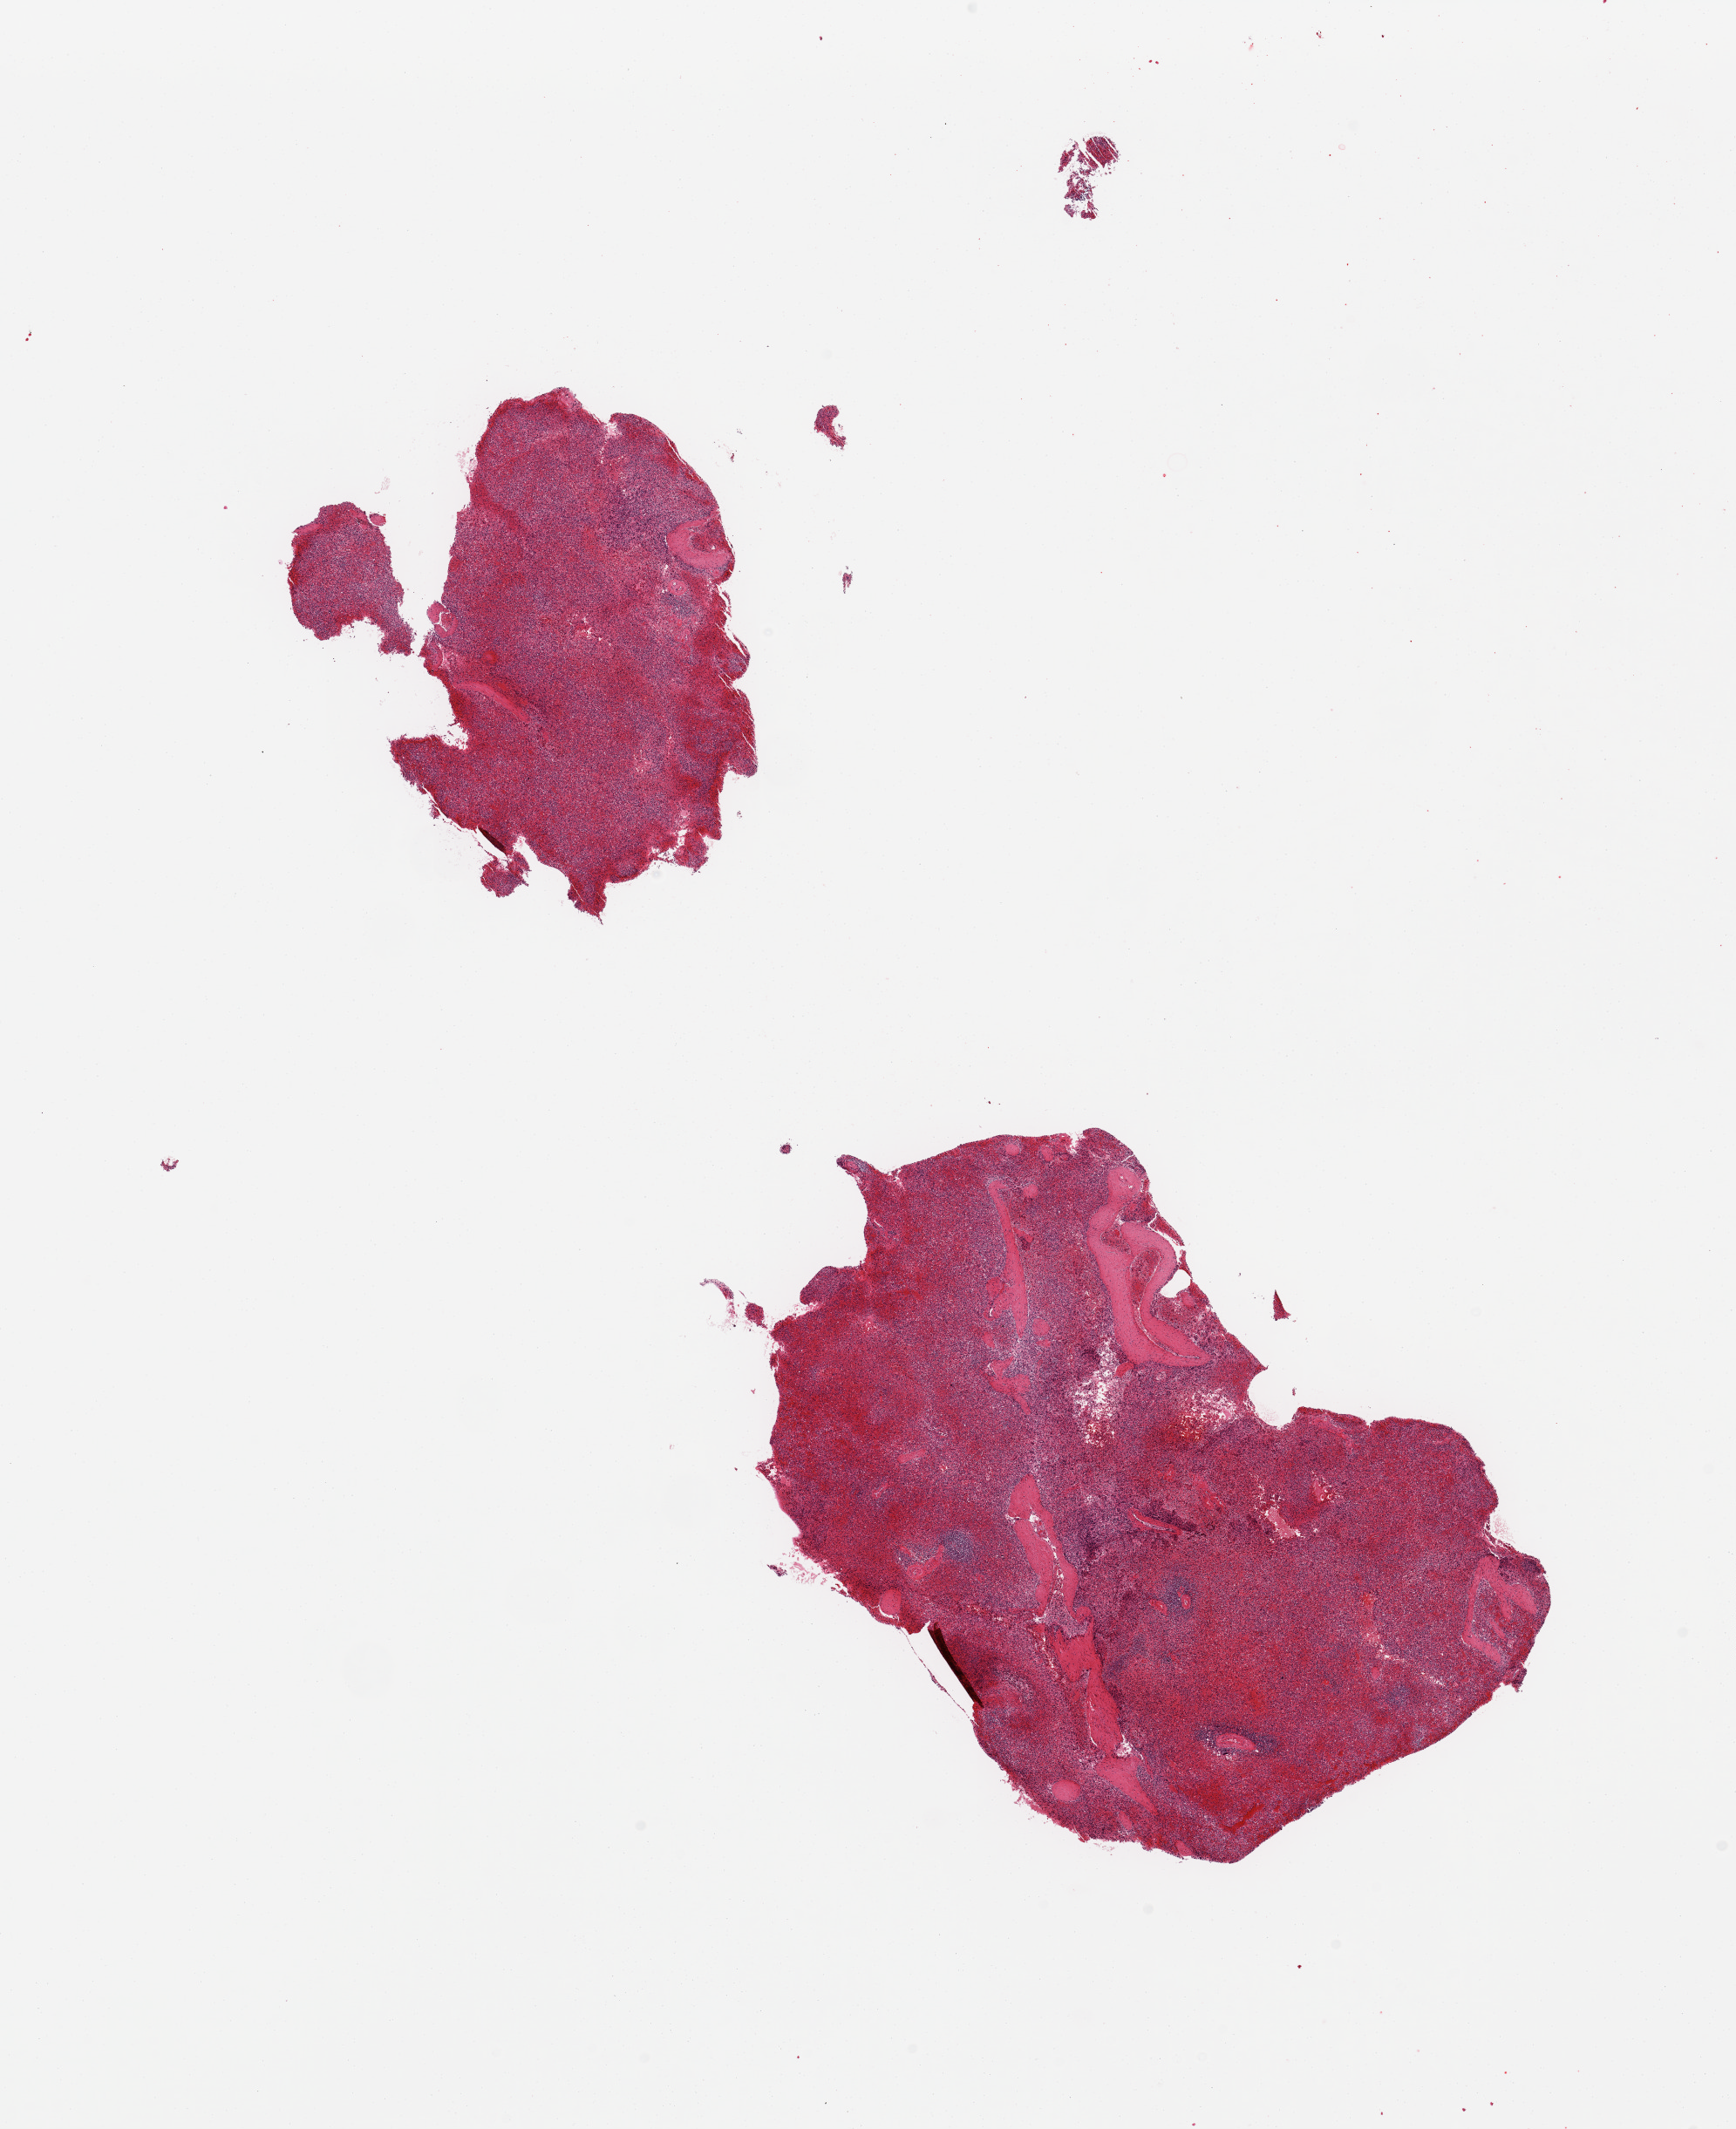
Haematoxylin and eosin whole-slide image, brightfield, a low-resolution overview of the entire scanned area, about 15.8 x 19.3 mm (from a 20x scan). PAXgene-fixed, paraffin-embedded tissue. Target tissue: spleen. Tissue donor sample. Donor: male.
* reviewer comment on this tissue sample: 2 pieces; severe congestion